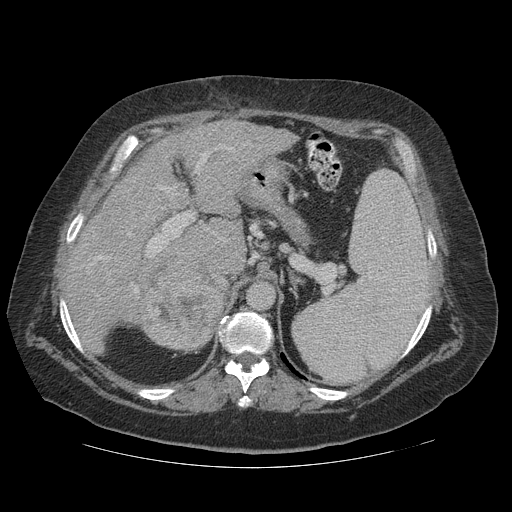
Contrast-enhanced abdominal CT (liver protocol), one axial slice. Position 77 of 121 along the scan axis. Reconstruction kernel STANDARD. 140 kVp. Soft-tissue window (W 400 / L 40 HU). 2.5 mm slice thickness. 512 × 512 image matrix, field of view 420 × 420 mm. From the clinical record (not read from this slice): diagnosis: hepatocellular carcinoma (patient treated with transarterial chemoembolisation; whether this scan precedes or follows treatment is not stated here); TNM stage (as recorded): Stage-IIIA; Child-Pugh class: A; tumour differentiation: well differentiated.
Structures marked on this image (semi-automatically segmented with operator editing):
- liver parenchyma outside the tumour (the mass and vessels are separate outlines, so this box may not span the whole liver): box from (x=64, y=120) to (x=296, y=338) px
- mass: (x=134, y=256)–(x=228, y=352)
- liver vessels: (x=88, y=142)–(x=250, y=321)